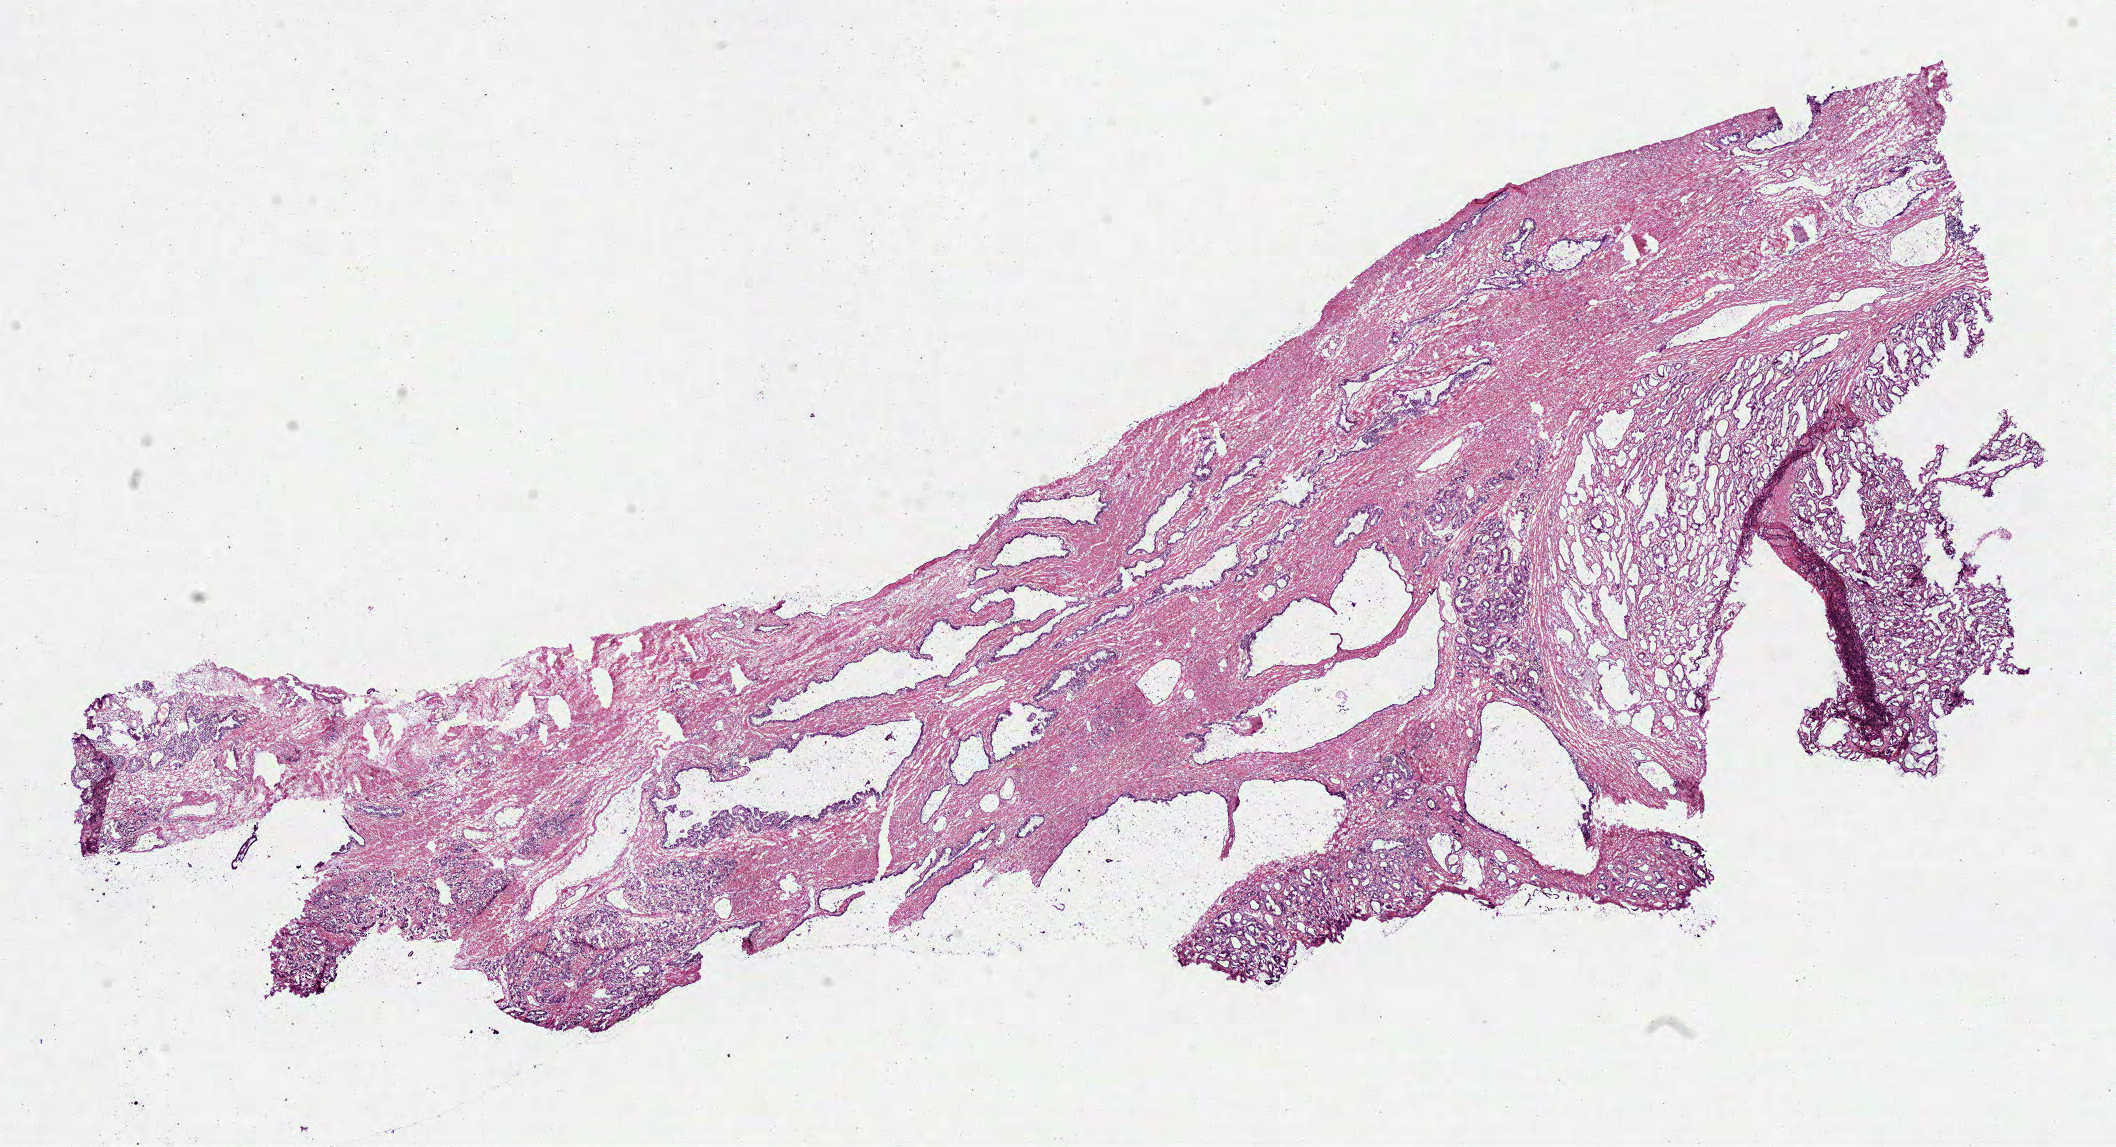
Digitized Hematoxylin and eosin (H&E) stained tissue section (whole slide) — a low-resolution overview of the entire scanned area, about 17.1 x 9.3 mm; frozen section from the bottom of the tissue portion; prostate, primary tumour sample. Male patient; age at initial diagnosis 71 years. Gleason score: 7 (3+4). Composition of this section per pathologist review: tumour cells 45%, tumour nuclei 45%, normal cells 25%, stromal cells 30%, necrosis 0%. Inflammatory infiltration, as recorded: lymphocyte infiltration 2%, monocyte infiltration 0%, neutrophil infiltration 0%.
Lymph nodes positive (case pathology): 0 of 13 examined. Laterality: bilateral. Diagnosis: Acinar cell carcinoma.